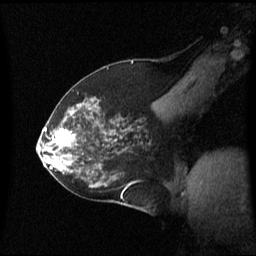
Breast MRI (dynamic contrast-enhanced), one sagittal slice; slice 36 of 60 in the series (ordered by position); dynamic contrast-enhanced series, image 2 of 3 at this slice position (ordered by acquisition); 1.5 T; TE 4.2 ms, TR 8.4 ms; 256 × 256 image matrix. Patient: female, 59 years. From the clinical record (not read from this slice): setting: breast cancer imaged before/during neoadjuvant chemotherapy; receptor status: HR-positive, HER2-negative.
Outlined on this slice (semi-automatically segmented with operator editing):
- analysis volume of interest (the breast-tissue region the enhancement analysis was run in; not a lesion): bounding box [x1, y1, x2, y2] px = [46, 114, 89, 163]
- tumour enhancement mask (voxels above the 70 % enhancement threshold inside the analysis volume of interest): [53, 130, 74, 147]